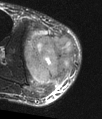
MRI of an extremity soft-tissue mass, one axial slice. Position 30 of 48 along the scan axis. T2-weighted fat-saturated. MR volume resampled by the dataset authors to the PET/CT grid (not the native acquisition matrix). 3.27 mm slice thickness. 102 × 119 image matrix, field of view 100 × 116 mm. Male patient. Case-level facts recorded for this patient, not image findings: histological type: pleiomorphic liposarcoma; grade: high; site of the primary tumour: right calf.
Annotated regions visible in this slice (expert contour drawn on MRI and transferred to this co-registered scan by the dataset authors):
- gross tumour volume including surrounding oedema: bounding box [x1, y1, x2, y2] px = [23, 28, 75, 88]
- gross tumour volume (mass): [23, 33, 77, 86]